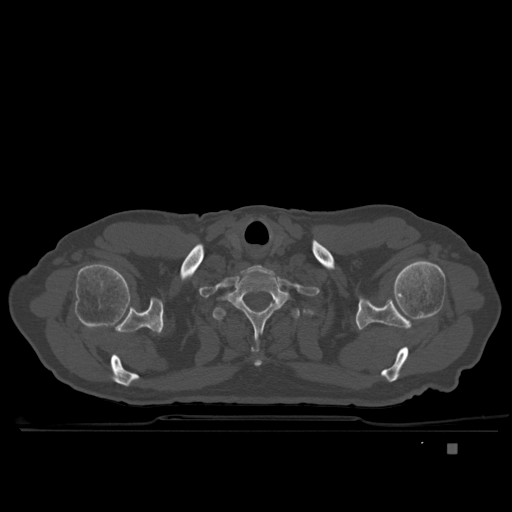
CT including the spine, one axial slice; position 323 of 435 along the scan axis; bone window (W 1800 / L 400 HU); 1.5 mm slice thickness; 512 × 512 image matrix. Male patient, age 73 years. From the clinical record (not read from this slice): primary cancer: skin.
Annotated regions visible in this slice (semi-automatically segmented with operator editing):
- T1 vertebra: bounding box [x1, y1, x2, y2] px = [220, 275, 291, 351]
- T2 vertebra: [214, 305, 300, 322]